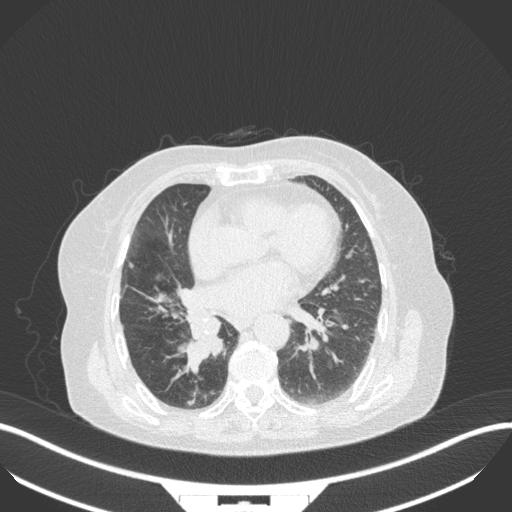
Chest CT, one axial slice; slice 139 of 329 in the series (ordered by position); reconstruction kernel B31f; lung window (W 1500 / L -600 HU); 512 × 512 image matrix, field of view 400 × 400 mm. Patient: female, 75 years. Case-level facts recorded for this patient, not image findings: clinical TNM (as recorded): T1b N0 M1a.
Structures marked on this image (rectangle marked by the reading radiologist):
- lung tumour (recorded histology: squamous cell carcinoma): bounding box [x1, y1, x2, y2] px = [174, 308, 226, 377]